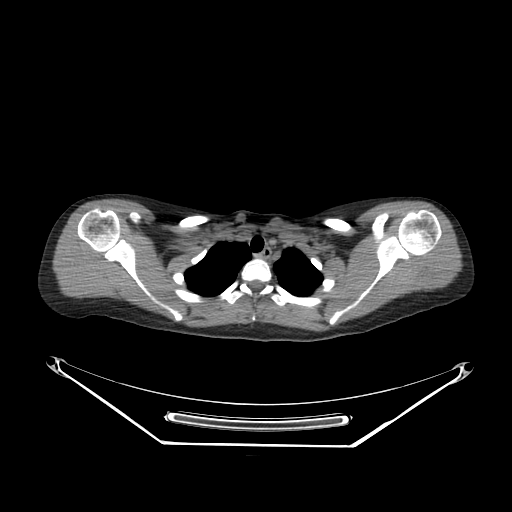
CT of an extremity soft-tissue mass (from a PET/CT study), one axial slice. Position 215 of 267 along the scan axis. Reconstruction kernel SOFT. Soft-tissue window (W 400 / L 40 HU). 3.75 mm slice thickness. 512 × 512 image matrix, field of view 500 × 500 mm. Female patient. From the clinical record (not read from this slice): histological type: malignant fibrous histiocytoma; grade: low; site of the primary tumour: left arm.
Annotated regions visible in this slice (expert contour drawn on MRI and transferred to this co-registered scan by the dataset authors):
- gross tumour volume (mass): bounding box [x1, y1, x2, y2] px = [425, 270, 437, 277]